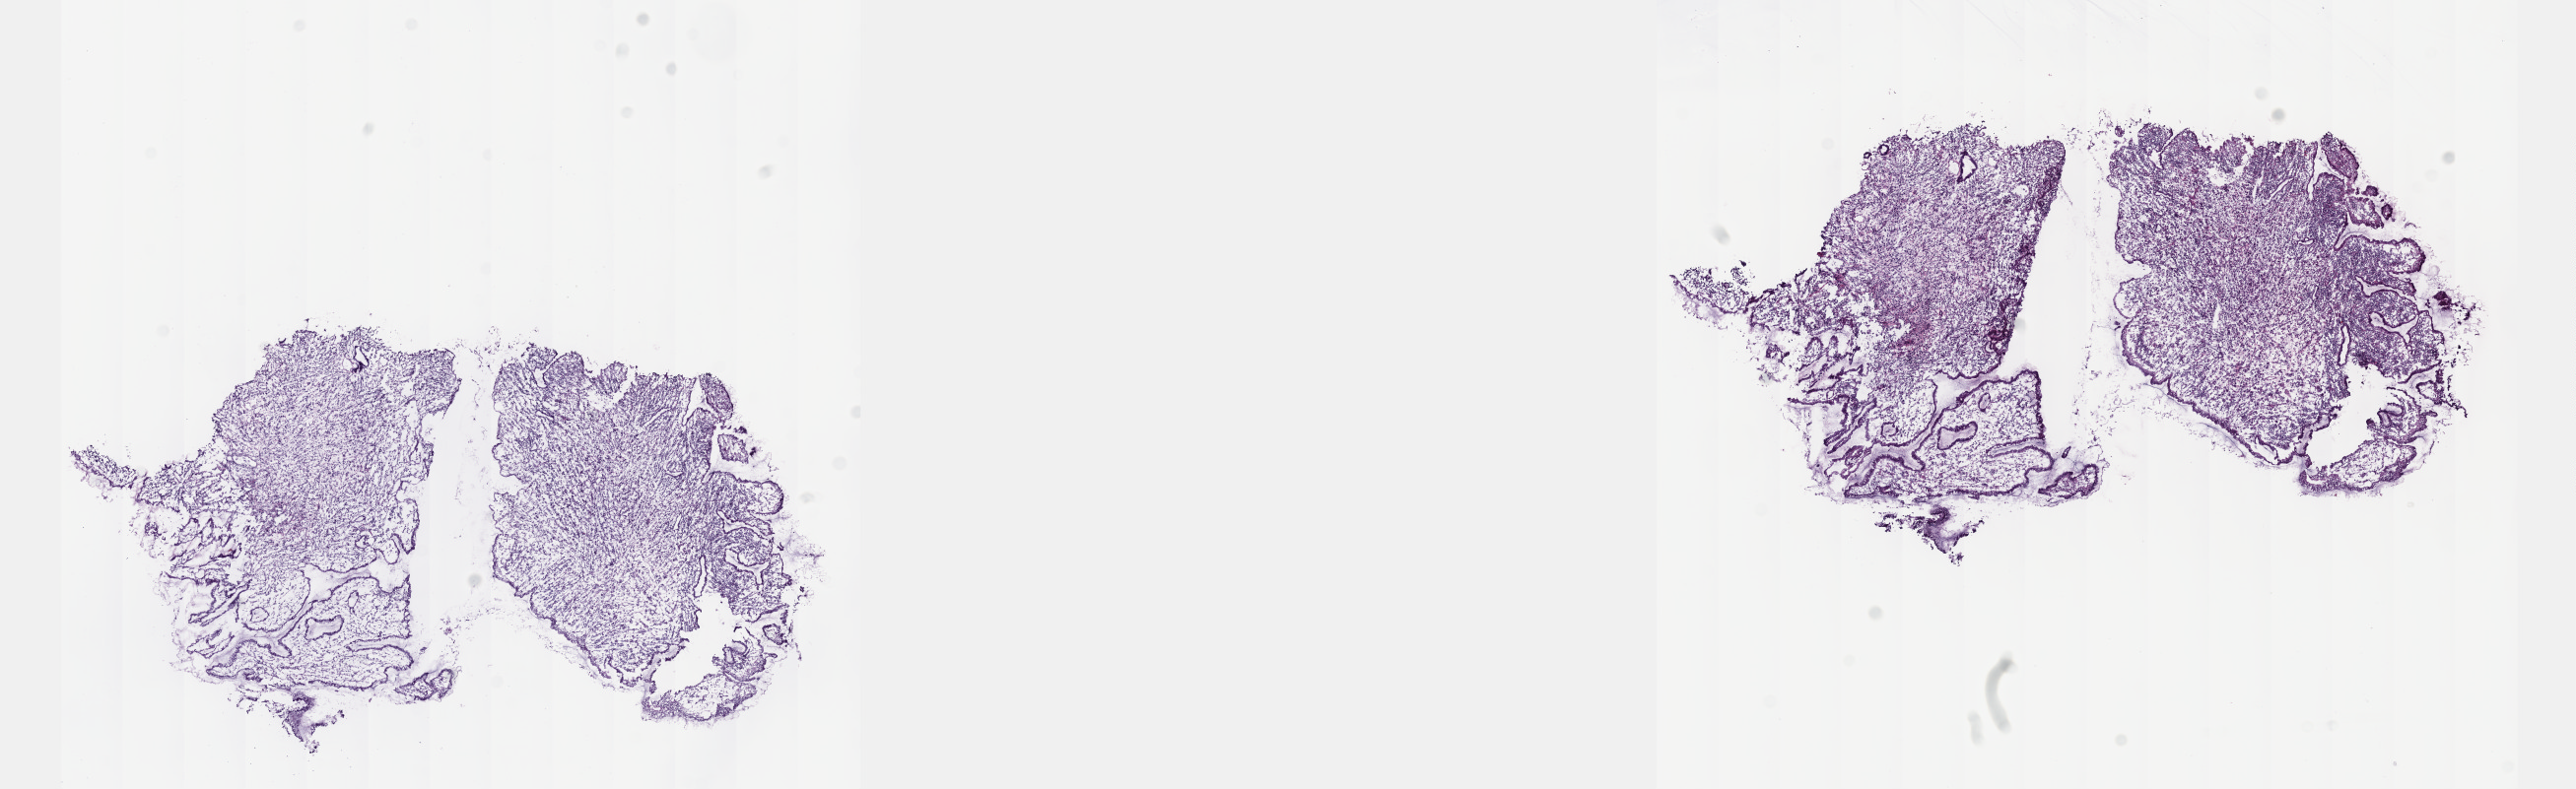
Digitized H&E-stained tissue section (whole slide), a low-resolution overview of the entire scanned area, about 21.1 x 6.5 mm. Frozen section from the top of the tissue portion. Stomach, primary tumour sample. Female patient; age at initial diagnosis 56 years. Histologic grade: G3 (poorly differentiated). Slide review estimates, as recorded: tumour cells 90%, tumour nuclei 65%, normal cells 10%, stromal cells 0%, necrosis 0%. Inflammatory infiltration, as recorded: lymphocyte infiltration 5%, monocyte infiltration 0%, neutrophil infiltration 0%.
AJCC pathologic stage: II (6th edition). Diagnosis: Signet ring cell carcinoma. TNM: T3 N0 M0.